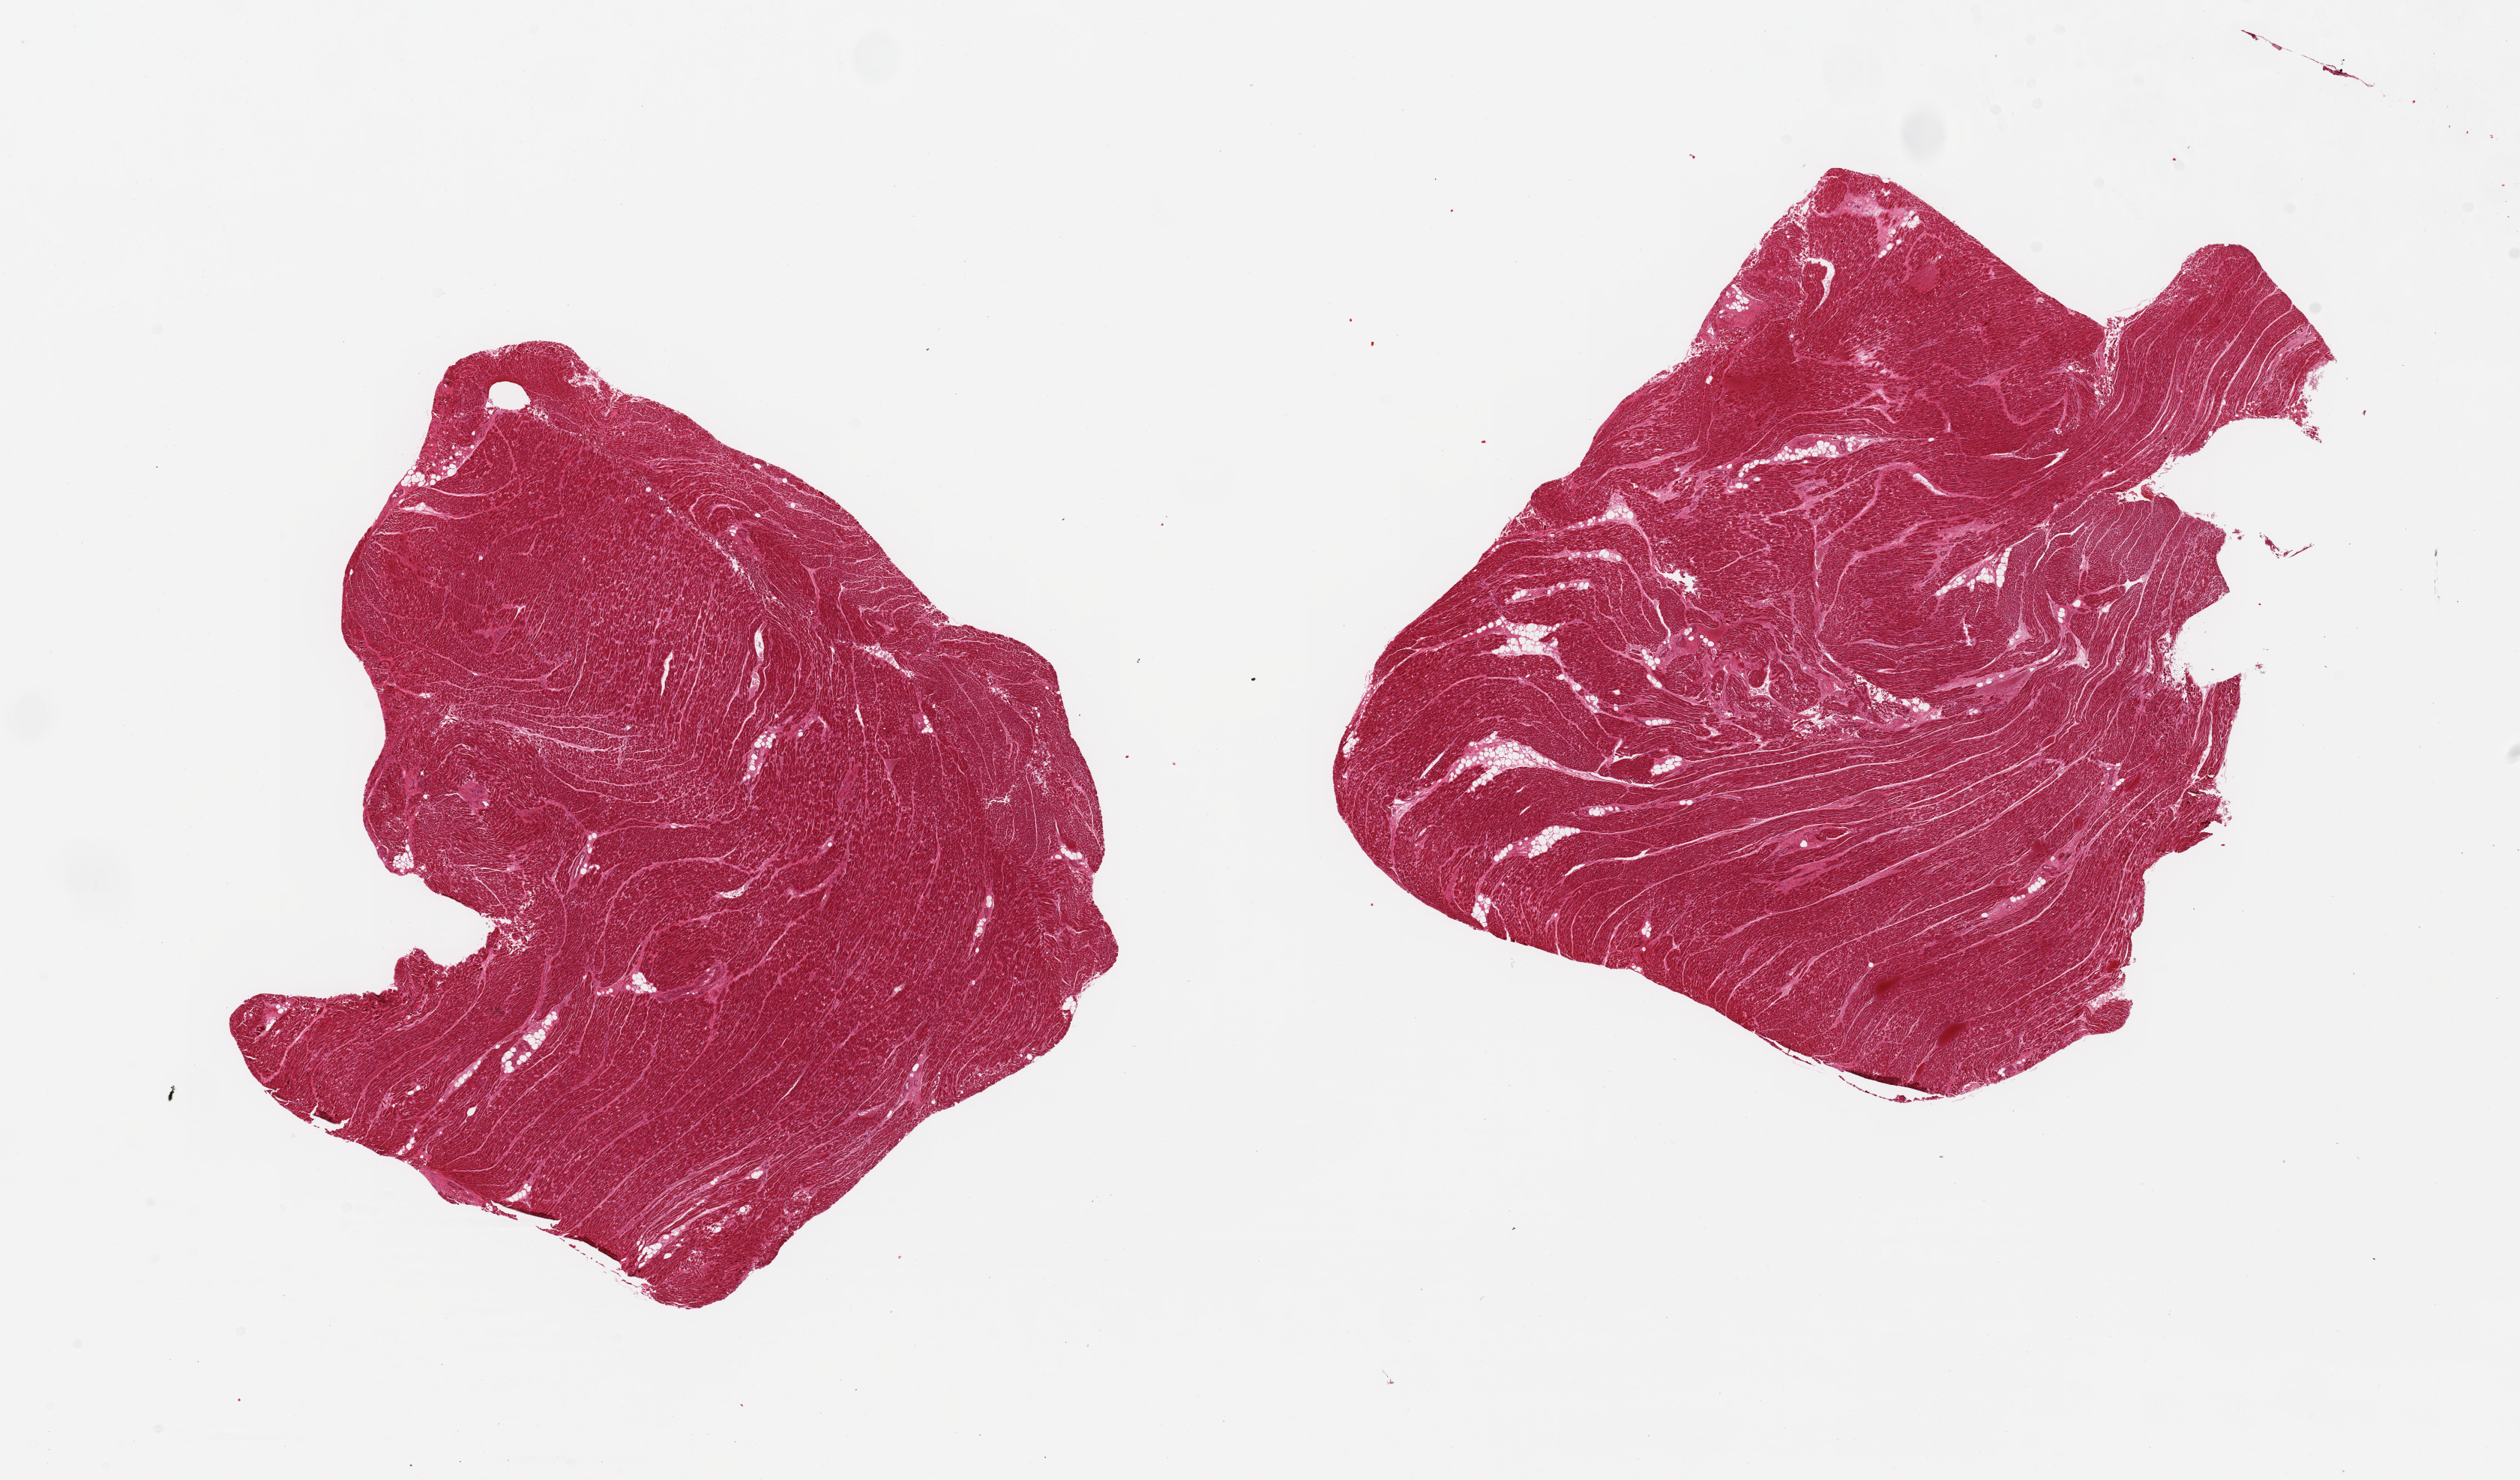
Digitized H&E-stained section, low-resolution overview of the scanned area, about 26.6 x 15.6 mm (acquisition: 20x scan); PAXgene-fixed paraffin-embedded (PFPE) section; sampled site (target tissue): heart; donor tissue sample. Male donor.
Pathologist's review note for this sample: 2 pieces; foci of hemorrhage and congestion <10%.